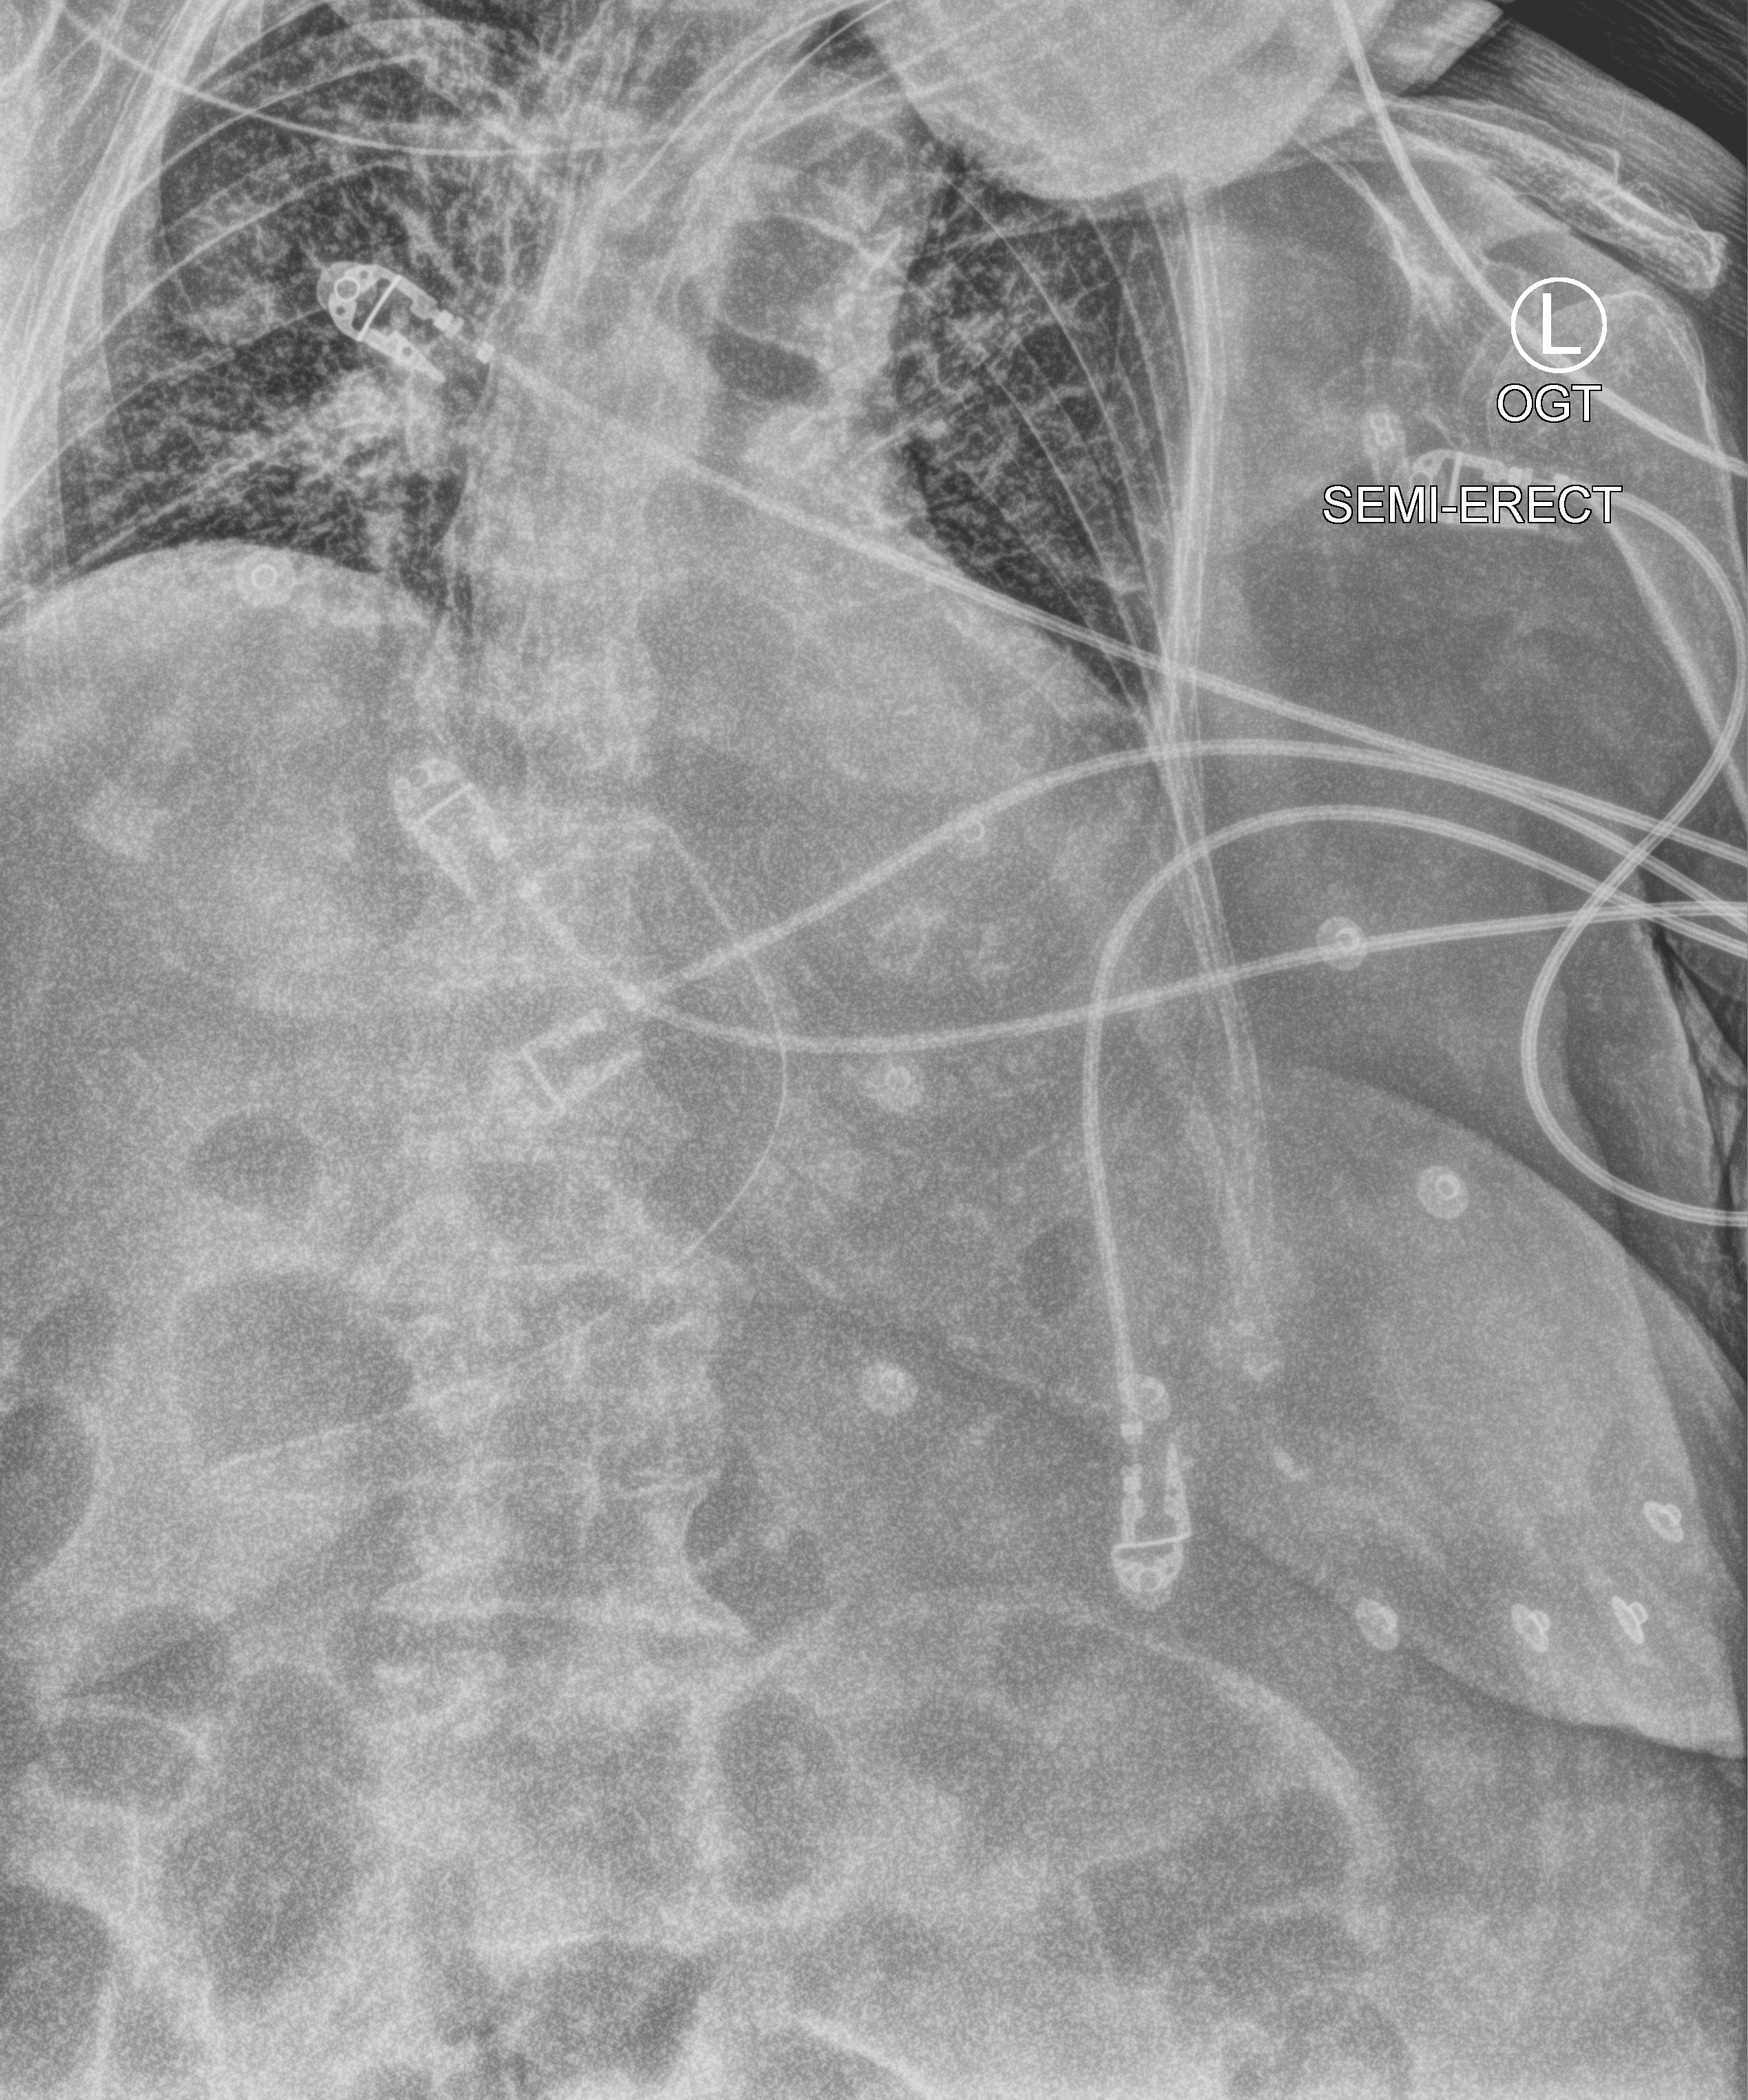
Bedside chest radiograph (computed radiography), anteroposterior (AP) projection. Female patient hospitalised with COVID-19, age 75–90 years.
From the hospital-stay record, not from the radiograph (when in the stay this image was taken is not recorded):
- other chronic lung disease (admission record): no
- mechanically ventilated during this hospital stay: yes